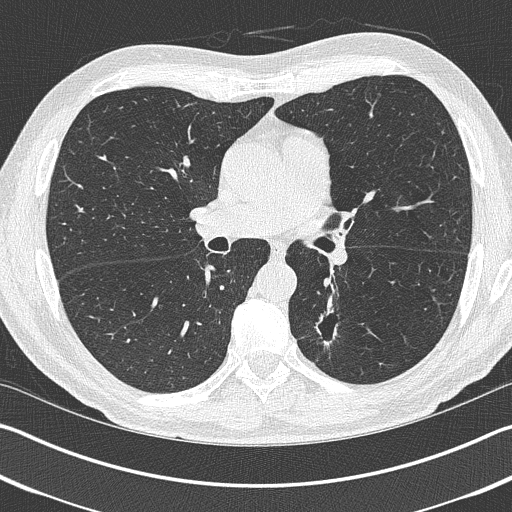
Low-dose screening chest CT, one axial slice; slice 235 of 402 in the series (ordered by position); reconstruction kernel B50f; lung window (W 1500 / L -600 HU); 512 × 512 image matrix, field of view 340 × 340 mm.
Annotated regions visible in this slice (manually delineated by an expert):
- lesion 1 (tumor, lower lobe of left lung): bounding box (x1, y1, x2, y2) in pixels: (315, 308, 338, 347)